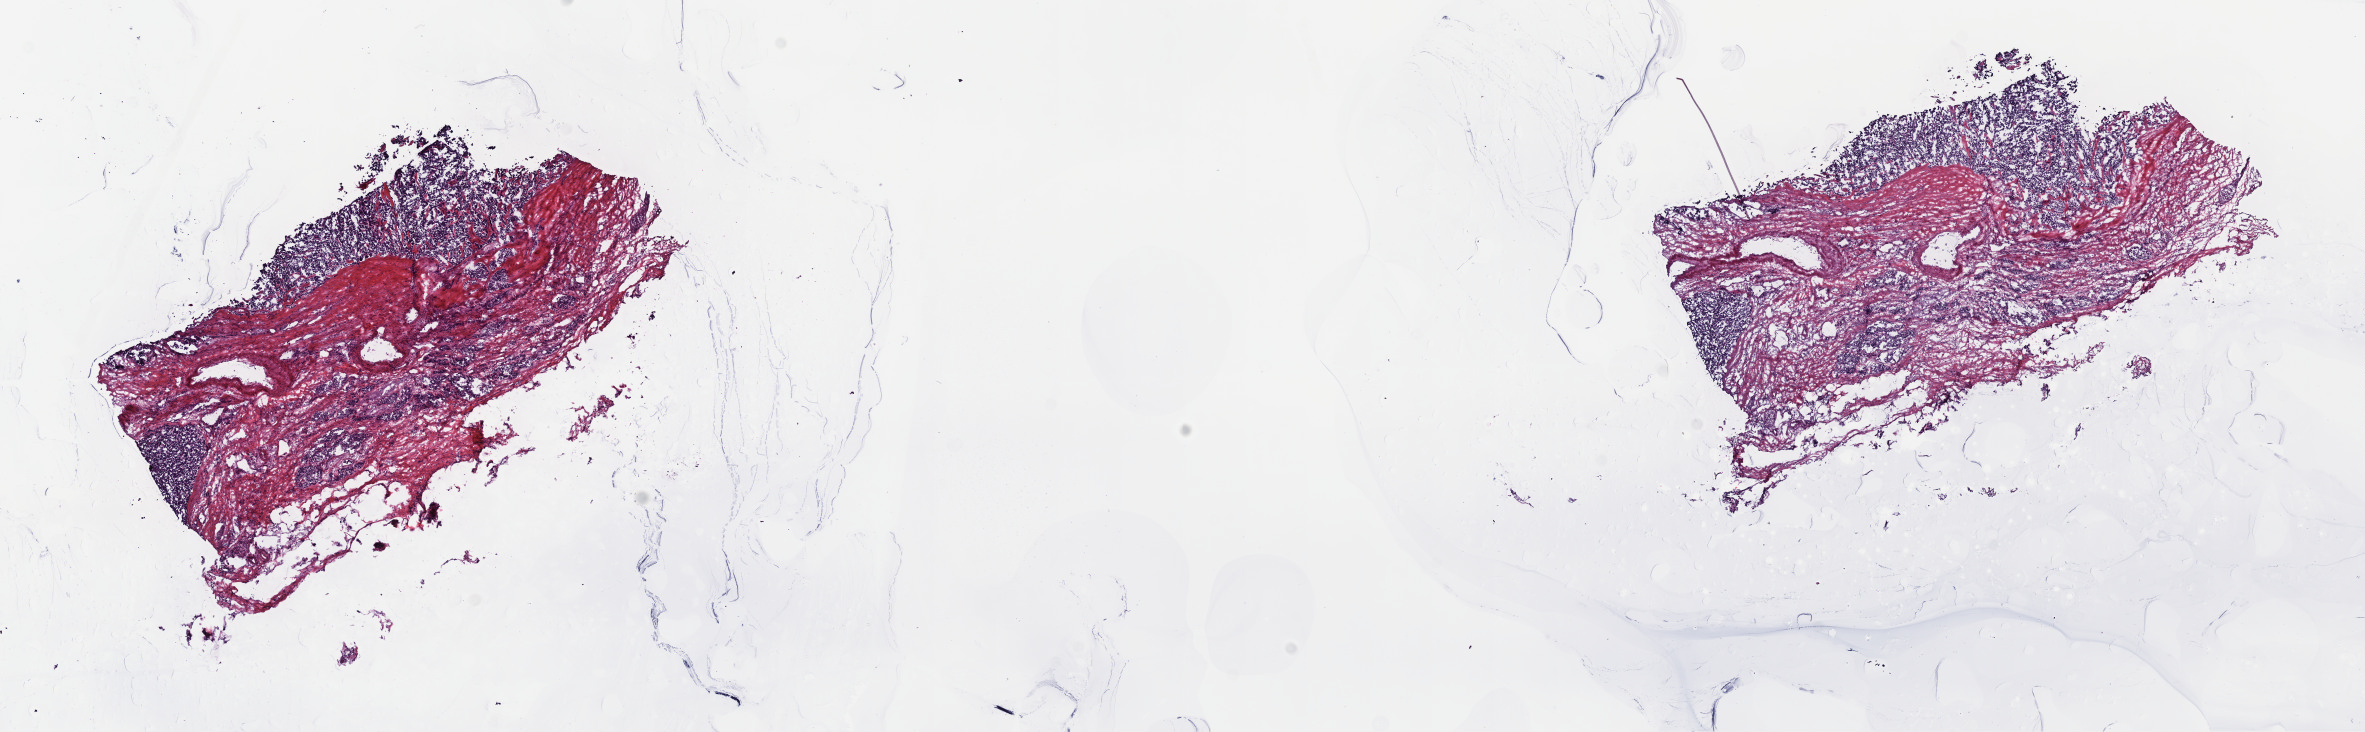
Whole-slide histology image, H&E, a low-resolution overview of the entire scanned area, about 19.1 x 5.9 mm (acquisition: 40x scan), frozen section from the top of the tissue portion, sample: primary tumour, pancreas. Patient: female, age at initial diagnosis 62 years. Histologic grade: G2 (moderately differentiated). Slide review estimates, as recorded: tumour cells 80%, tumour nuclei 65%, normal cells 0%, stromal cells 20%, necrosis 0%. Infiltration values recorded for this section: lymphocyte infiltration 0%, monocyte infiltration 0%, neutrophil infiltration 0%.
- AJCC pathologic stage: IB (6th edition)
- diagnosis: Neuroendocrine carcinoma, NOS (body of pancreas)